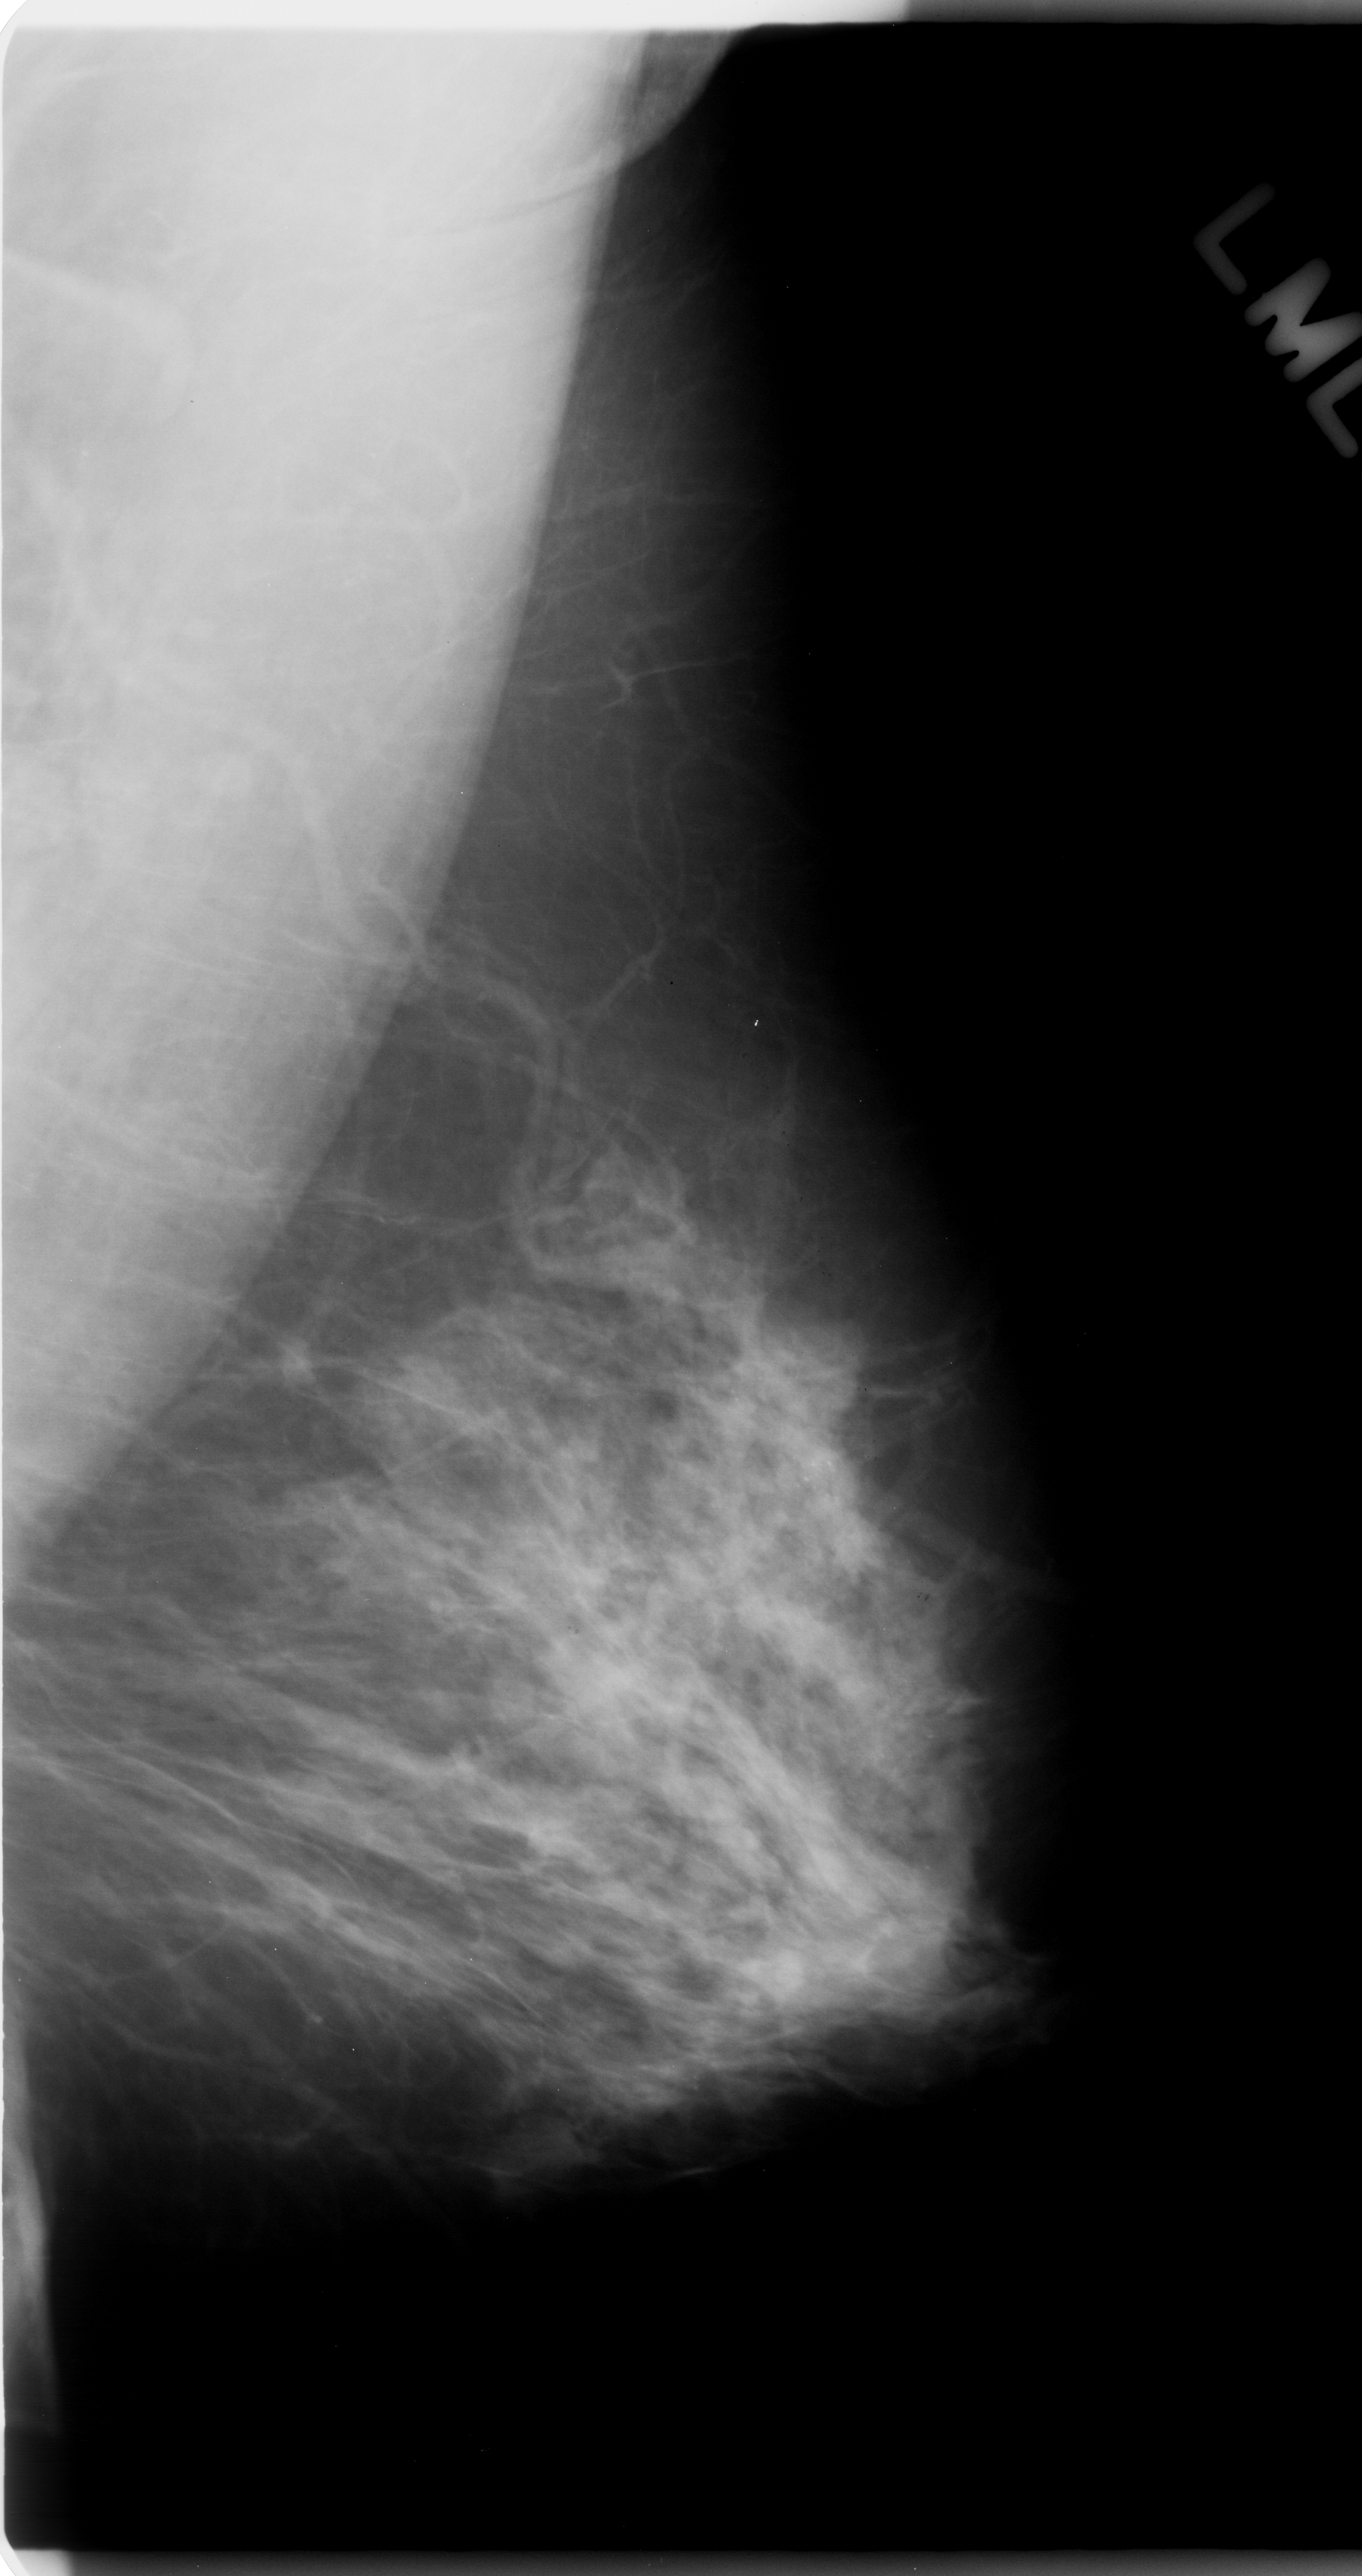
Mammogram (digitized film). Left breast. MLO view. Breast composition: scattered fibroglandular densities (BI-RADS density category 2 of 4). 1362 × 2576 image matrix.
Expert-marked regions of interest on this image (one box per marked abnormality):
- calcifications, morphology amorphous, distribution regional; BI-RADS assessment category 4; pathology result (as recorded, not read from the image): malignant: bounding box [x1, y1, x2, y2] px = [652, 1252, 1004, 1854]